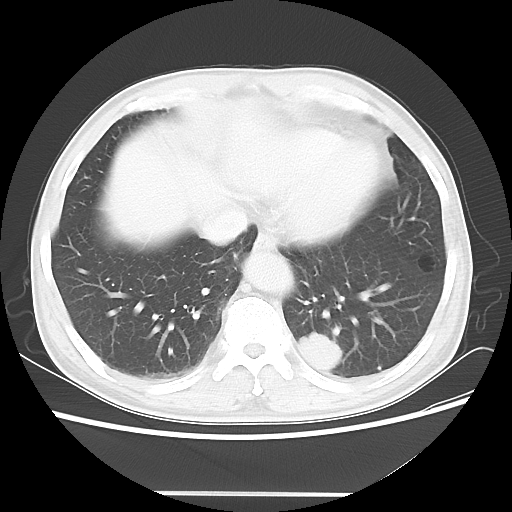
Chest CT, one axial slice. Position 15 of 60 along the scan axis. Lung window (W 1500 / L -600 HU). 512 × 512 image matrix, field of view 360 × 360 mm. Patient: male, 55 years. Case-level facts recorded for this patient, not image findings: clinical TNM (as recorded): T1c N3 M0; histopathological grade: G3.
Structures marked on this image (bounding box drawn by a radiologist):
- lung tumour (recorded histology: small cell carcinoma): box from (x=292, y=329) to (x=349, y=378) px